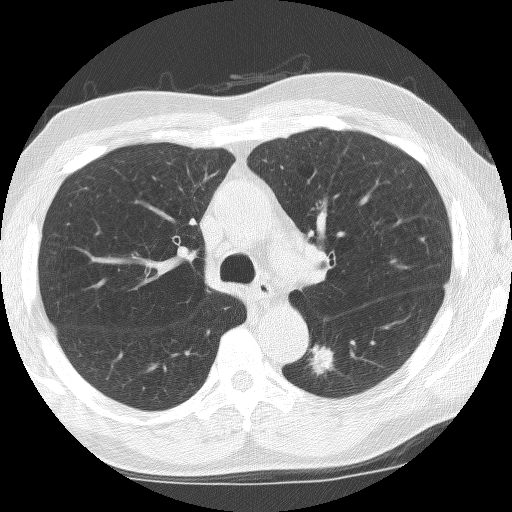
Chest CT (low-dose screening protocol), one axial image. First (baseline) screen. Lung window (W 1500 / L -600 HU). Slice 56 of 155 in the series. Male, age 67 years at enrolment. Current smoker at enrolment.
- Expert reader's lesion annotation, bounding box (x1, y1, x2, y2) in pixels: (295, 339, 341, 389).
- Screening reader's record for this exam (one nodule recorded; not confirmed to be the boxed lesion): non-calcified nodule or mass ≥4 mm, left lower lobe, 18 × 13 mm, spiculated (stellate) margins, soft tissue attenuation.
- Later outcome: lung cancer diagnosed 5 days after this screen — non-small cell carcinoma, left lower lobe, undifferentiated (G4), stage IA (AJCC 6th edition), 12 mm at pathology.